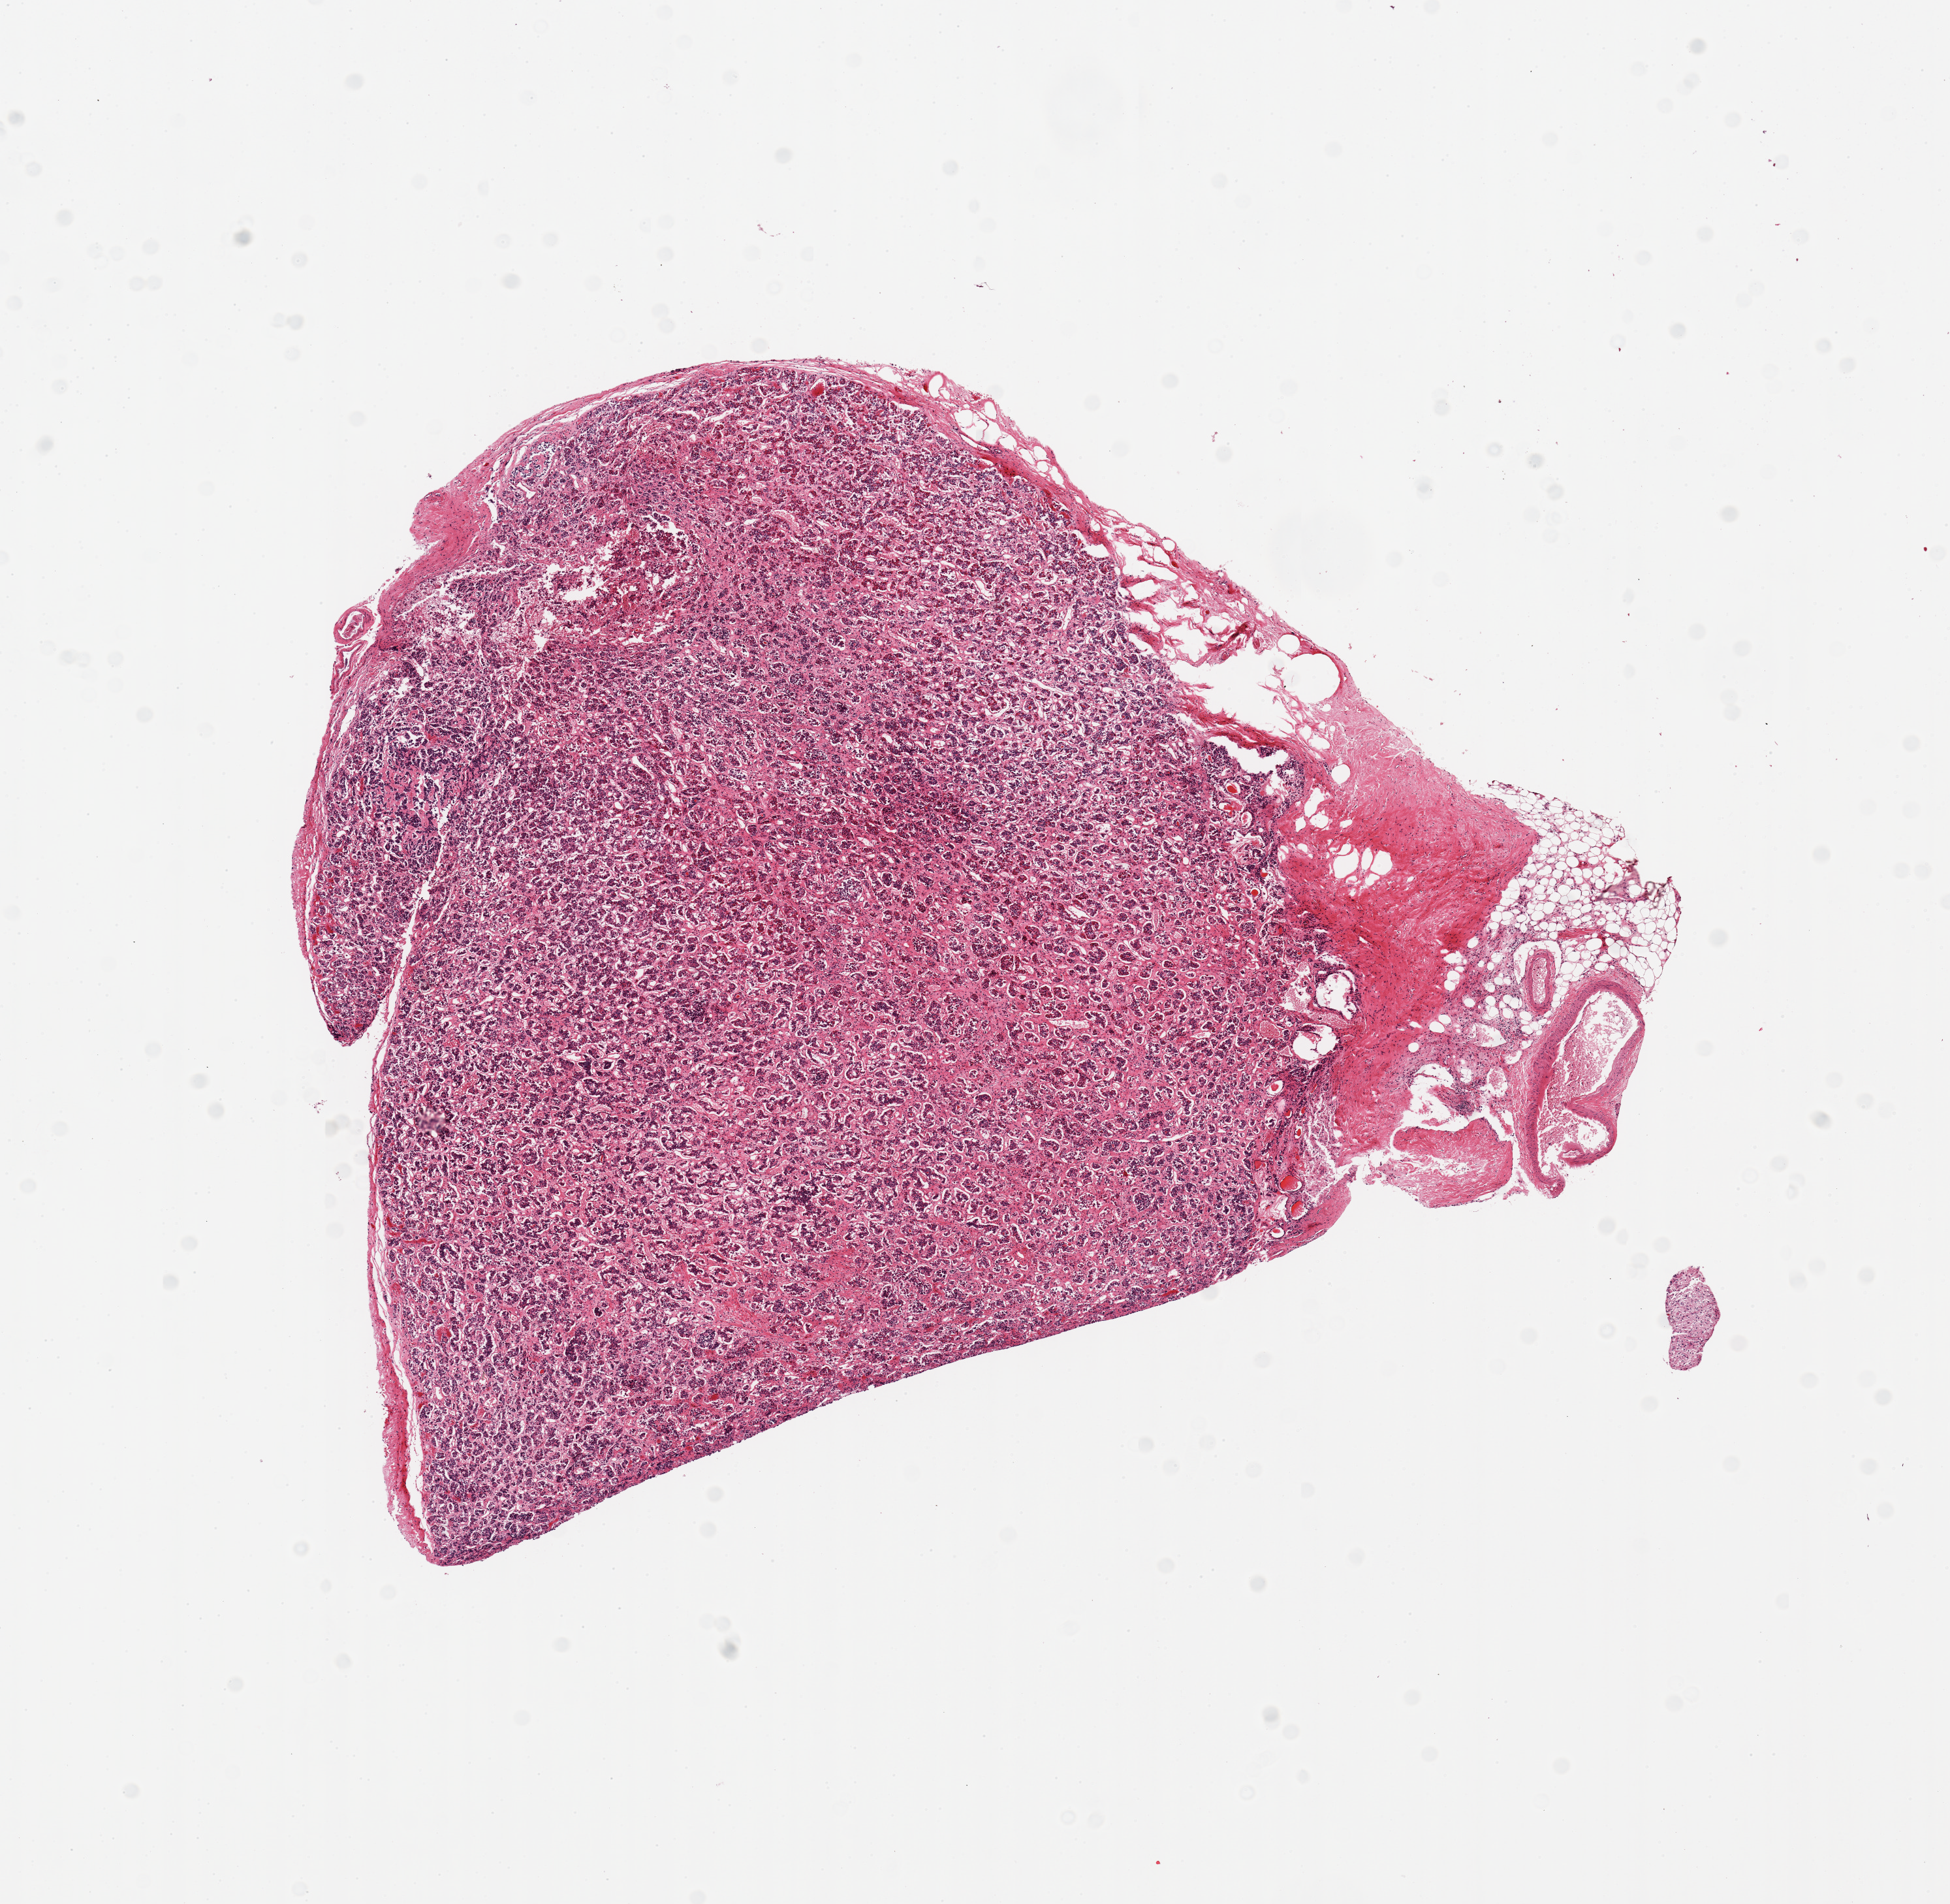
Whole-slide image, H&E stain, brightfield — whole scanned area (about 11.8 x 11.5 mm) shown as a low-resolution overview; PAXgene-fixed, paraffin-embedded tissue; target tissue: pituitary; donor tissue sample. Male donor.
* reviewer comment on this tissue sample: 1 piece; adenohypophysis